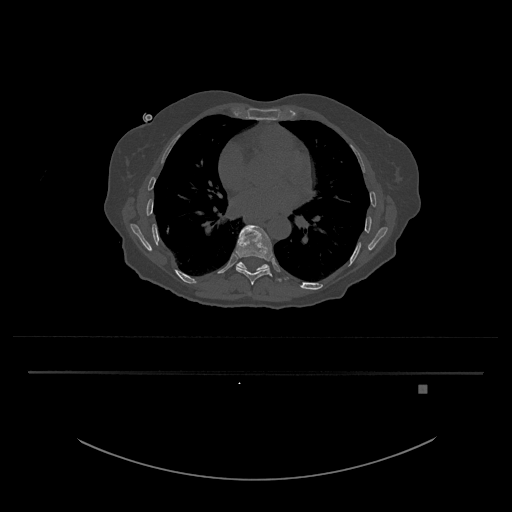
CT including the spine, one axial slice. Reconstruction kernel Br40s/3. 120 kVp. Bone window (W 1800 / L 400 HU). 0.5 mm slice thickness. 512 × 512 image matrix, field of view 500 × 500 mm. Female patient, age 57 years. From the clinical record (not read from this slice): primary cancer: cervical.
Structures marked on this image (semi-automatically segmented with operator editing):
- T10 vertebra: bounding box [x1, y1, x2, y2] px = [236, 262, 270, 272]
- T9 vertebra: [236, 225, 273, 285]